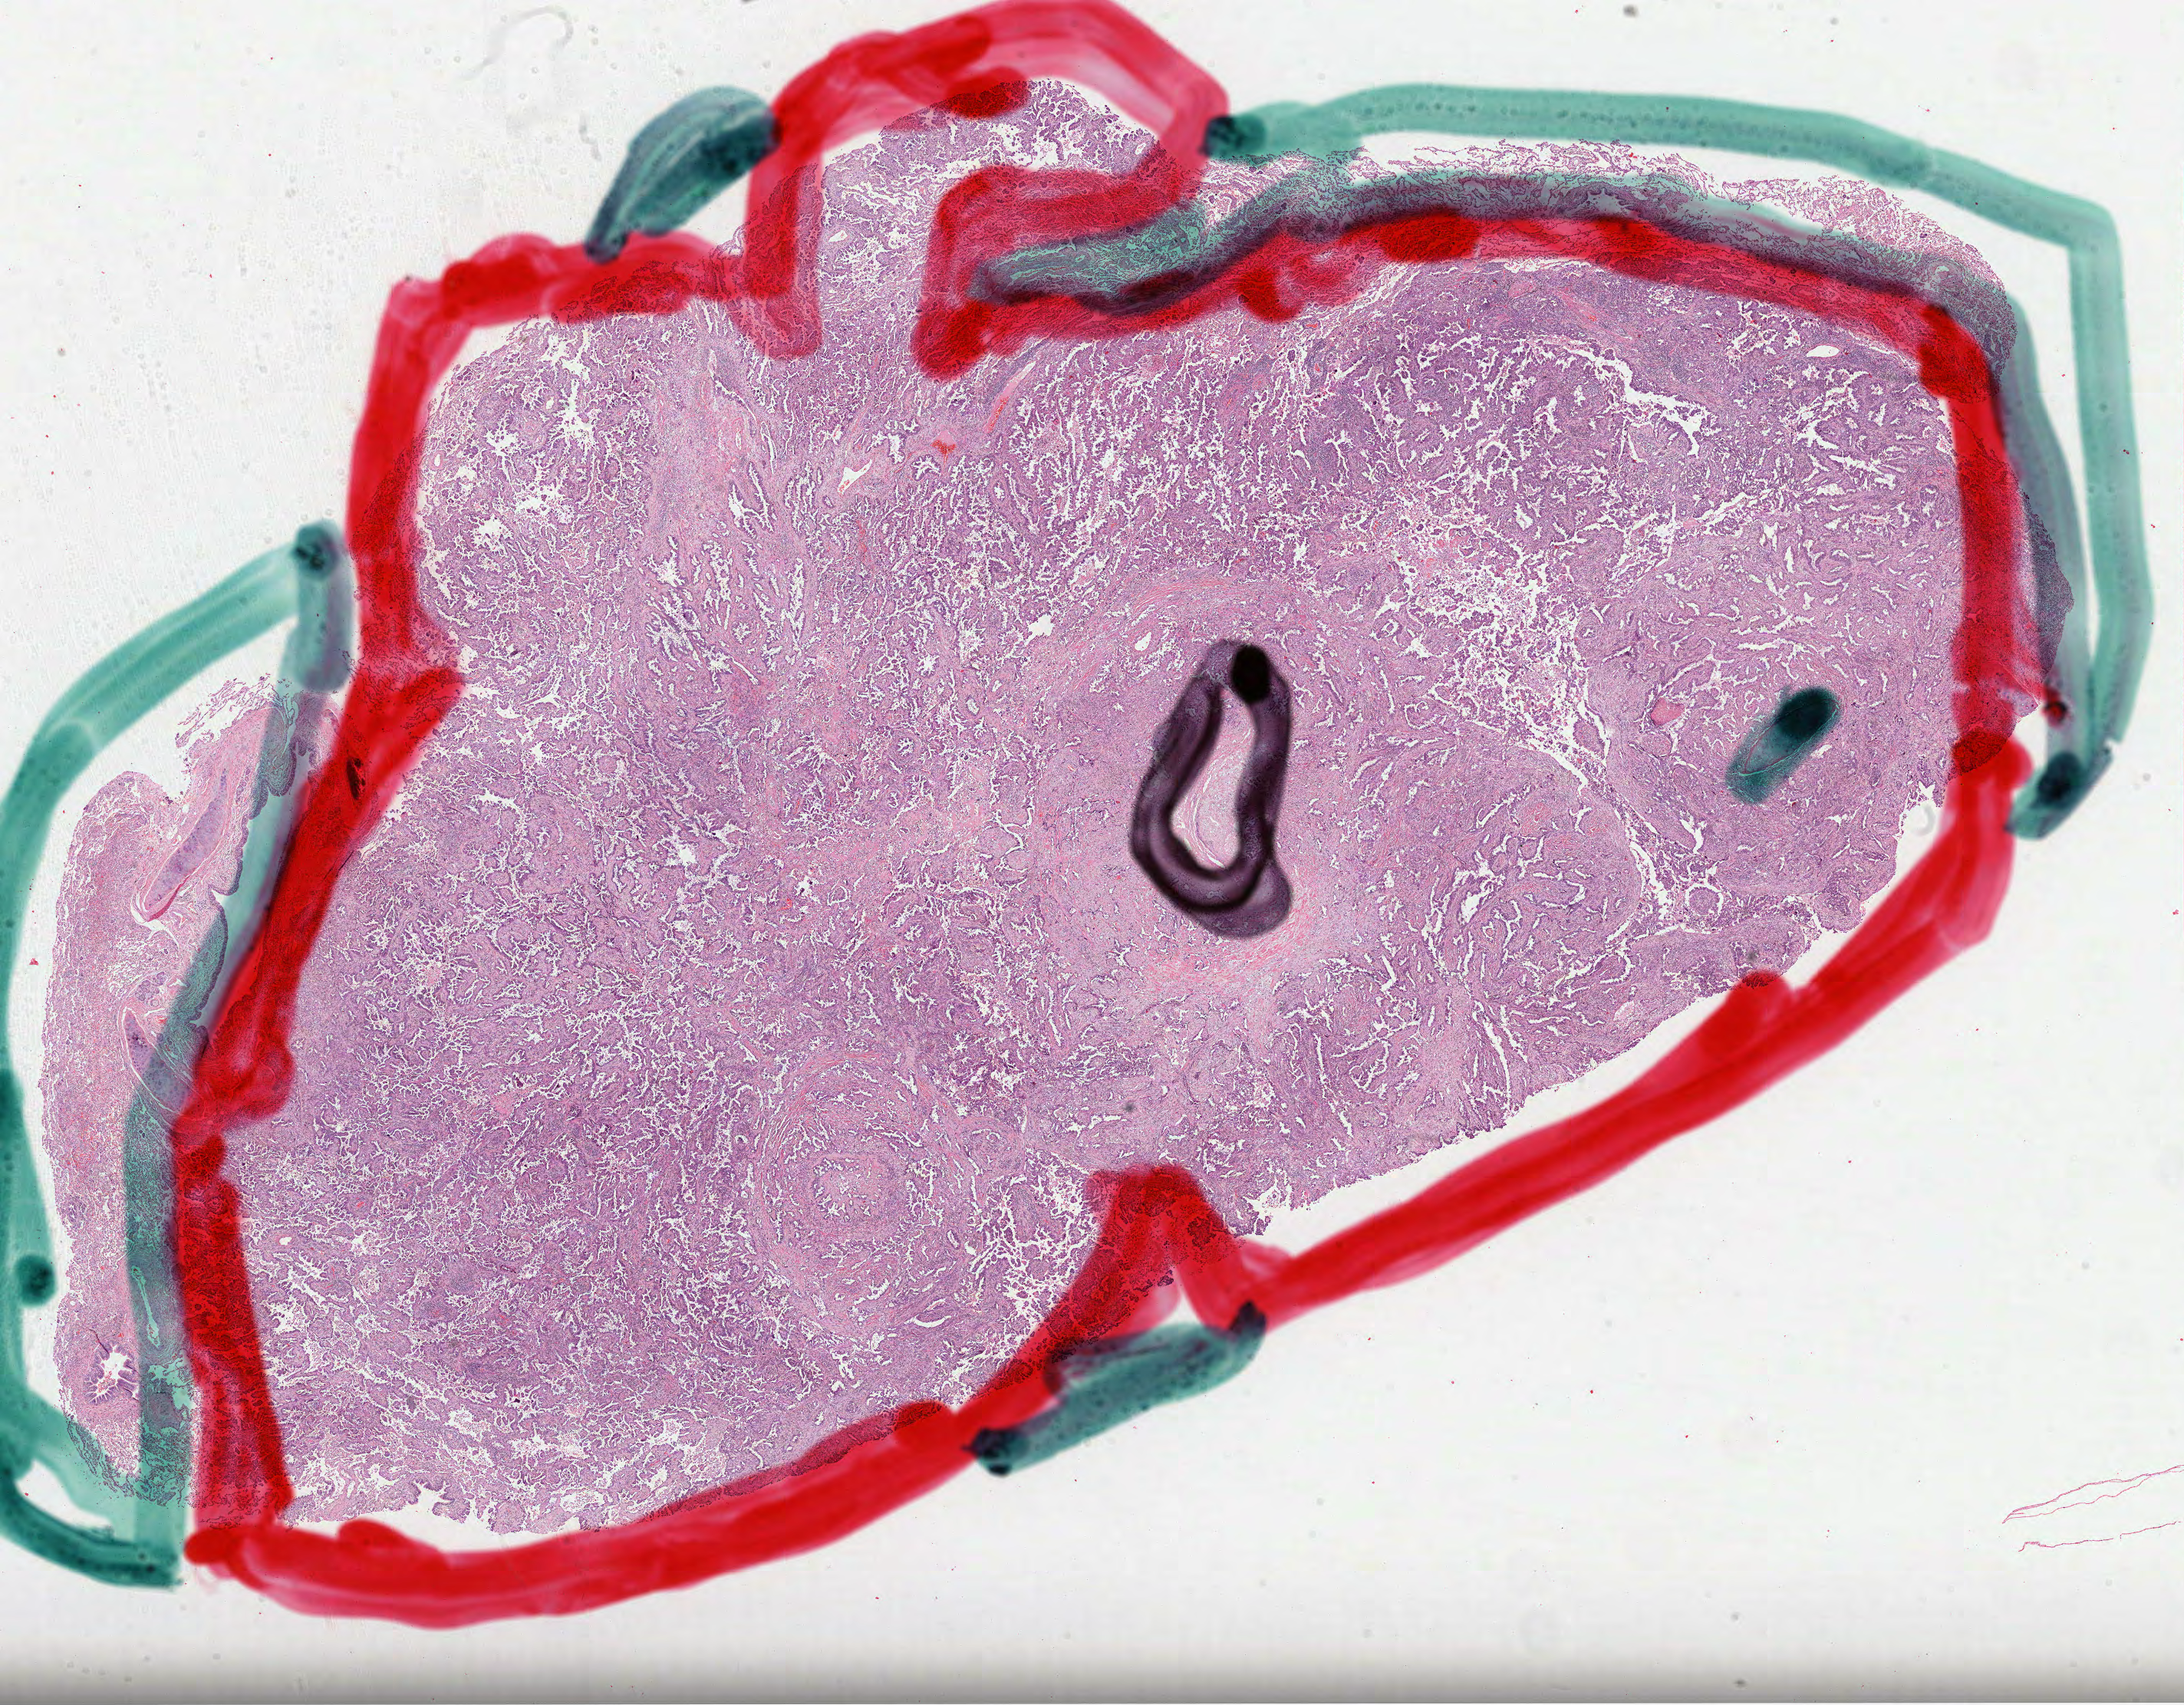
Digitized Hematoxylin and eosin (H&E) stained tissue section (whole slide), a low-resolution overview of the entire scanned area, about 23.0 x 17.9 mm. Formalin-fixed paraffin-embedded (FFPE) diagnostic section. Sample: primary tumour, lung. Female, age 62 years at initial diagnosis.
- pathologic diagnosis: Papillary adenocarcinoma, NOS (lower lobe, lung)
- laterality: left
- TNM: T1b N1 M0
- AJCC pathologic stage: IIA (7th edition)